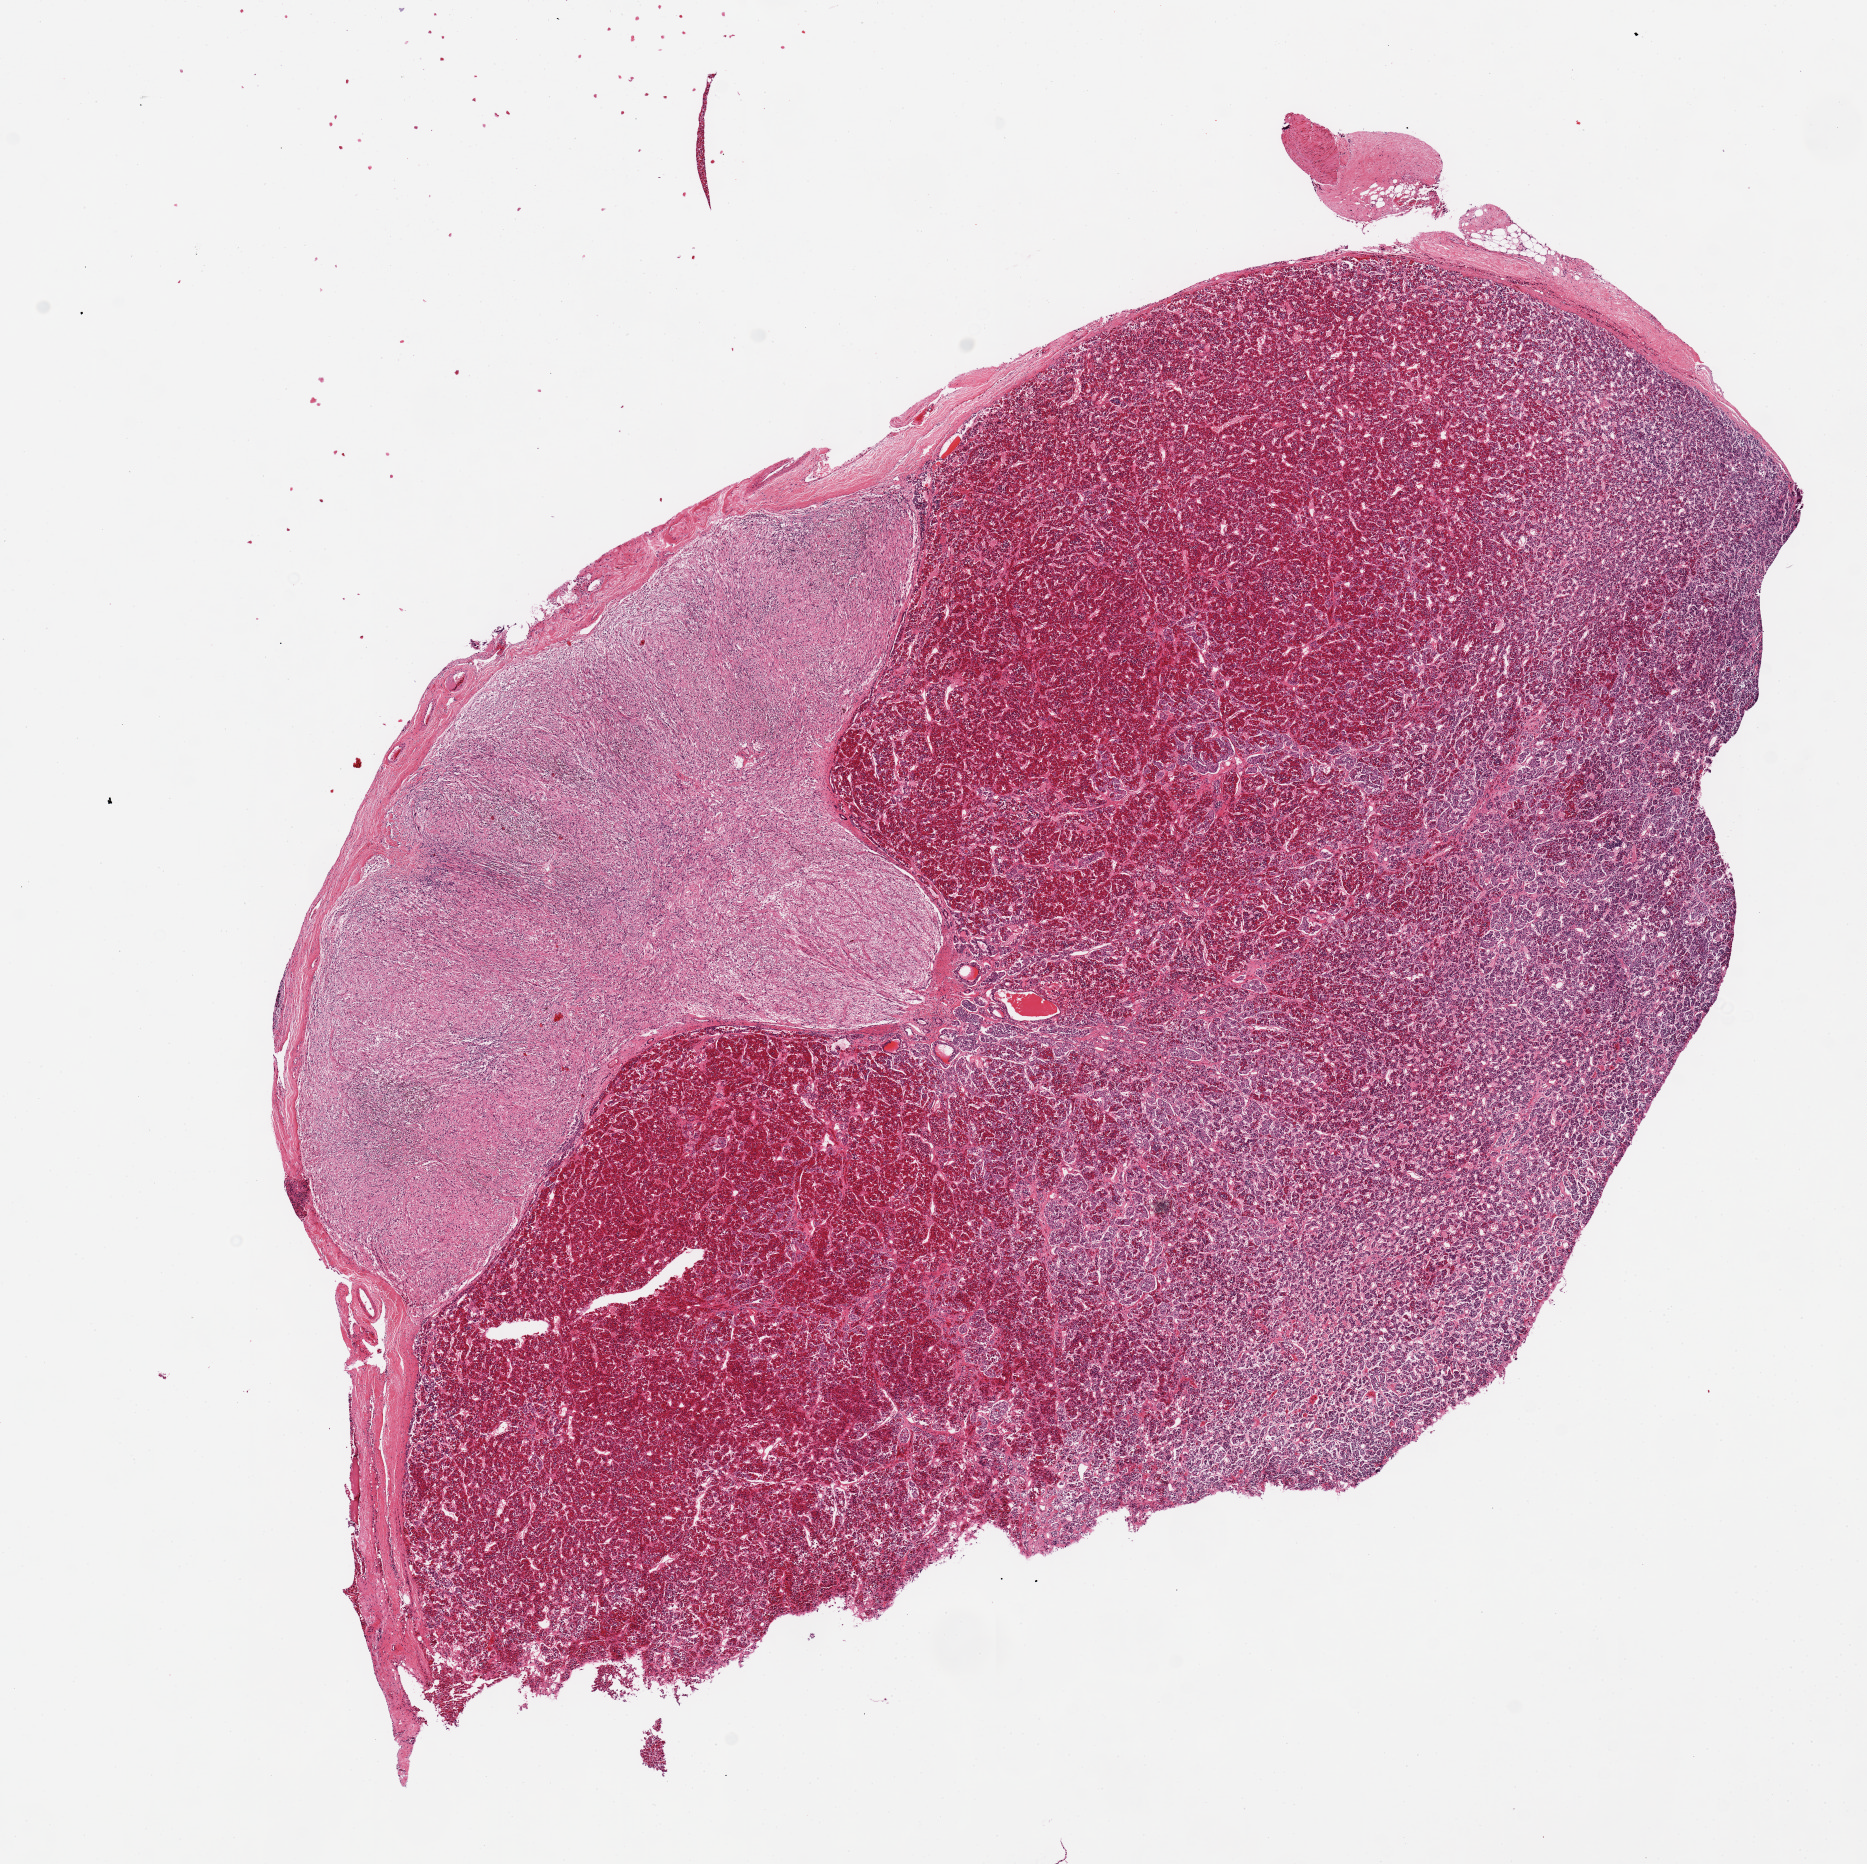
Whole-slide image, hematoxylin and eosin (H&E) stain, brightfield, whole scanned area (about 14.8 x 14.7 mm, slide scanned at 20x) shown as a low-resolution overview; PAXgene-fixed paraffin-embedded (PFPE) section; target tissue: pituitary; tissue donor sample. Donor sex: male.
Reviewer comment on this tissue sample: 1 pieces: anterior and posterior.